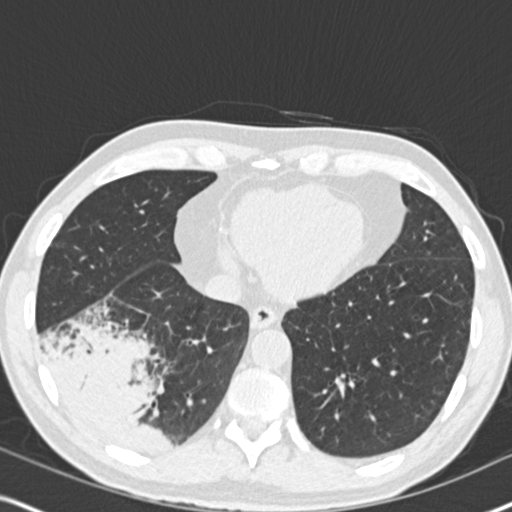
Low-dose screening chest CT, one axial slice. Lung window (W 1500 / L -600 HU). 2 mm slice thickness. 512 × 512 image matrix, field of view 330 × 330 mm.
Annotated regions visible in this slice (expert manual segmentation):
- lesion 1 (tumor, lower lobe of right lung): box from (x=47, y=327) to (x=169, y=455) px